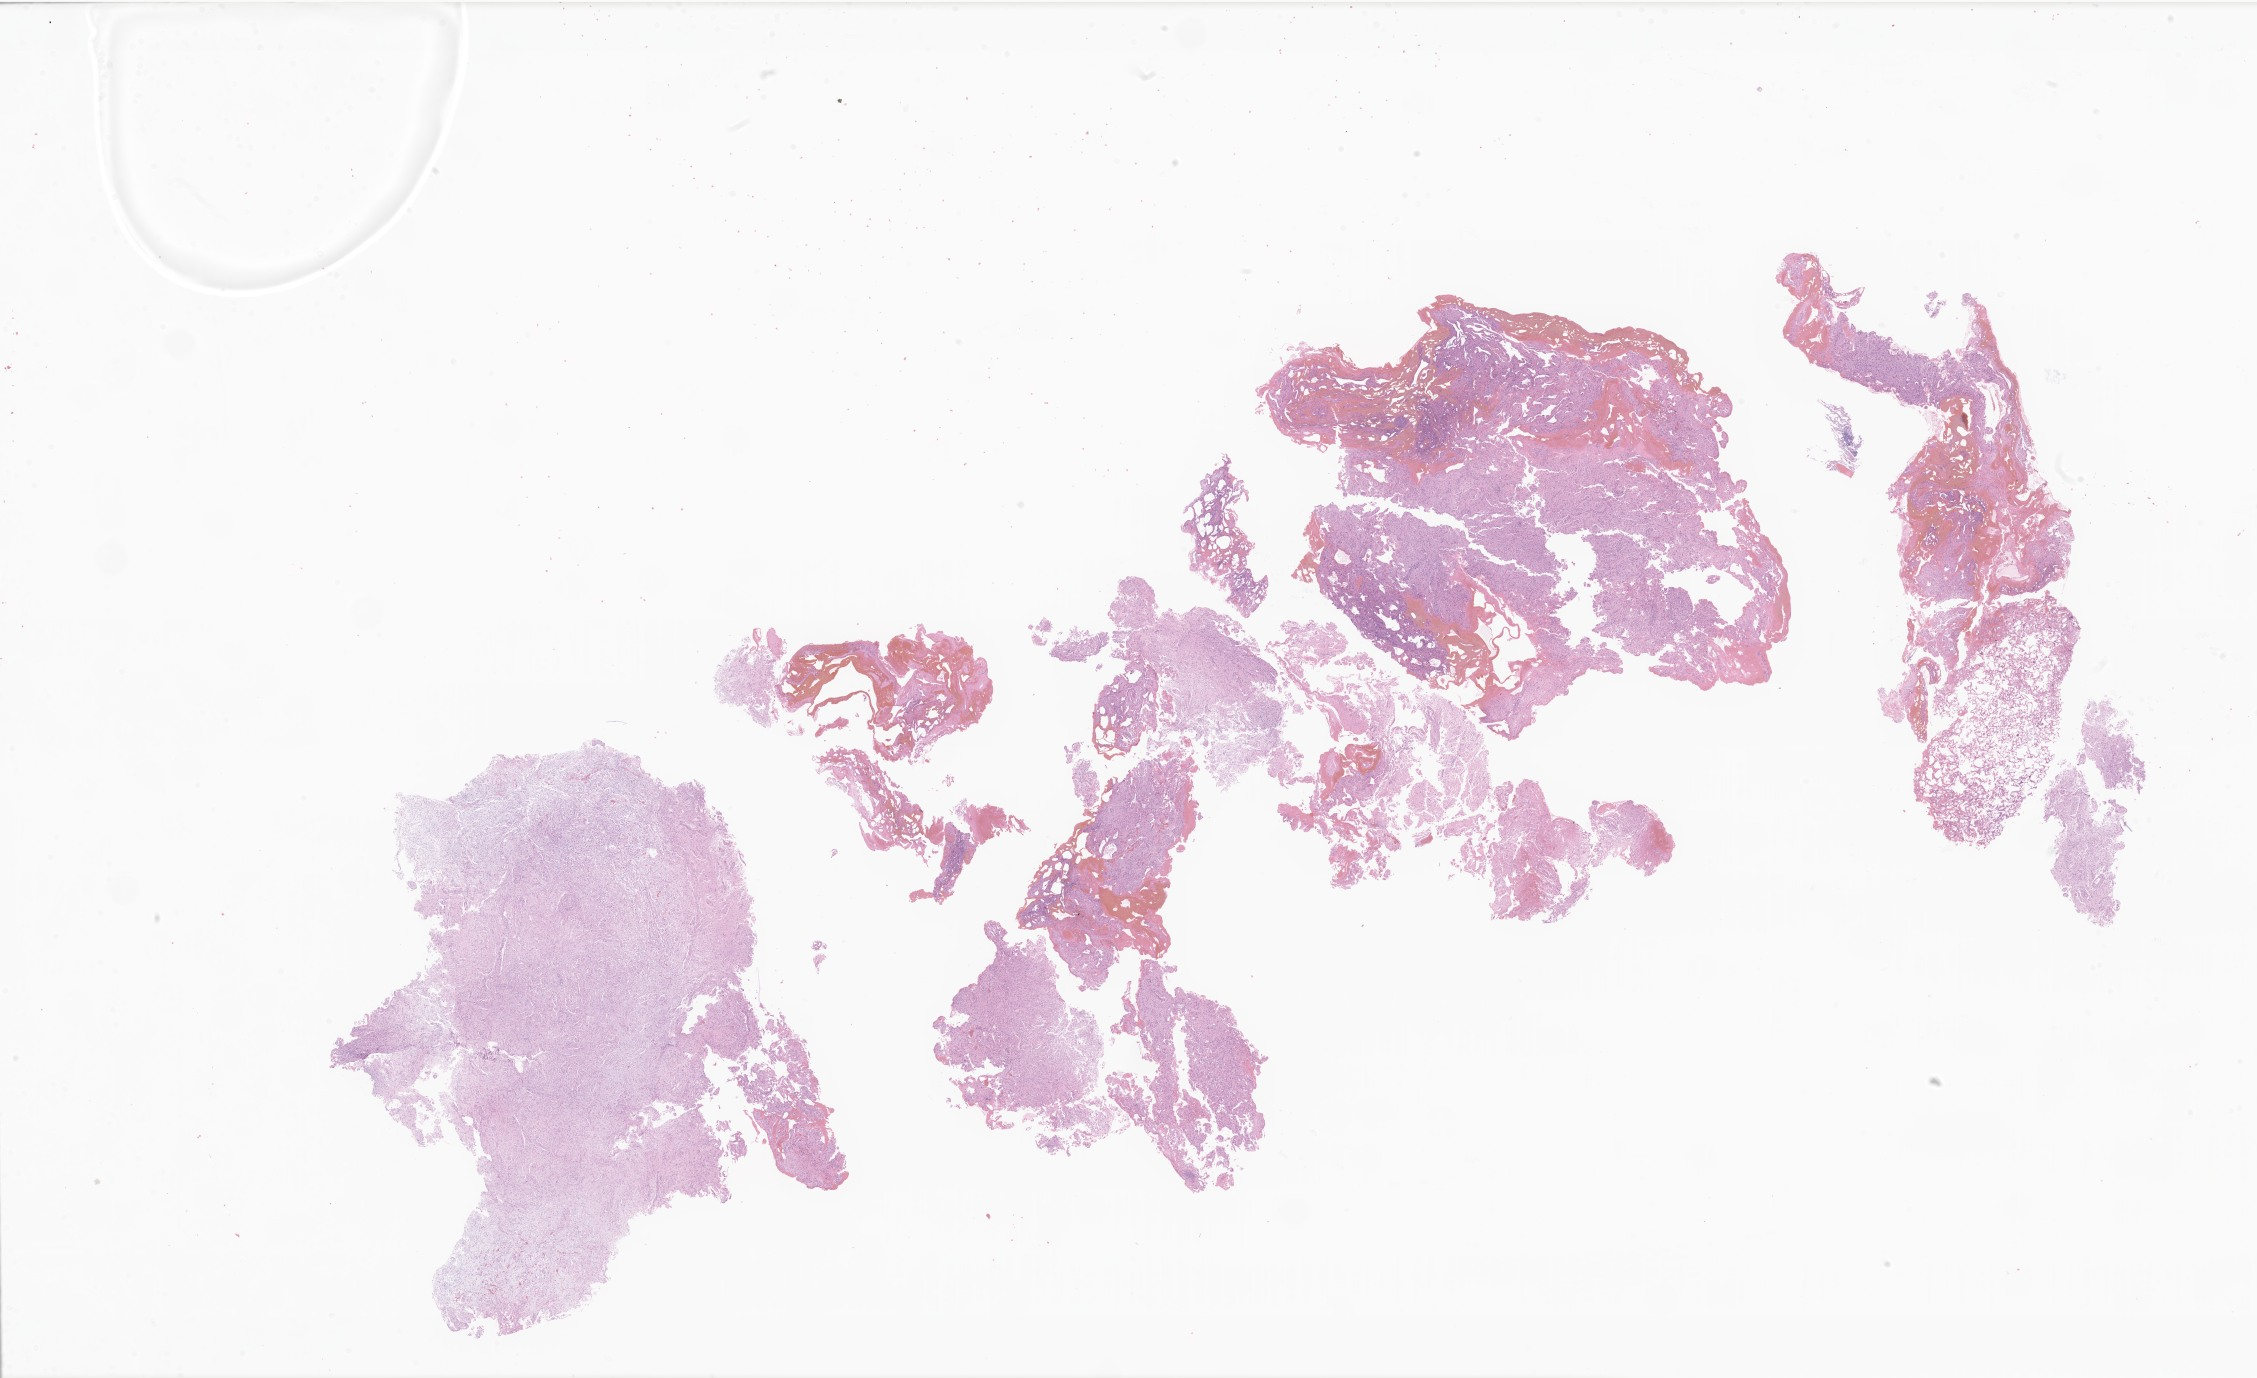
H&E whole-slide image of tumor tissue from the brain, low-resolution overview of the scanned area, about 38.1 x 23.2 mm; formalin-fixed paraffin-embedded section. Patient: male, age 67 months (5 years 7 months).
Diagnosis (ICD-O-3 morphology term): Pilocytic astrocytoma.